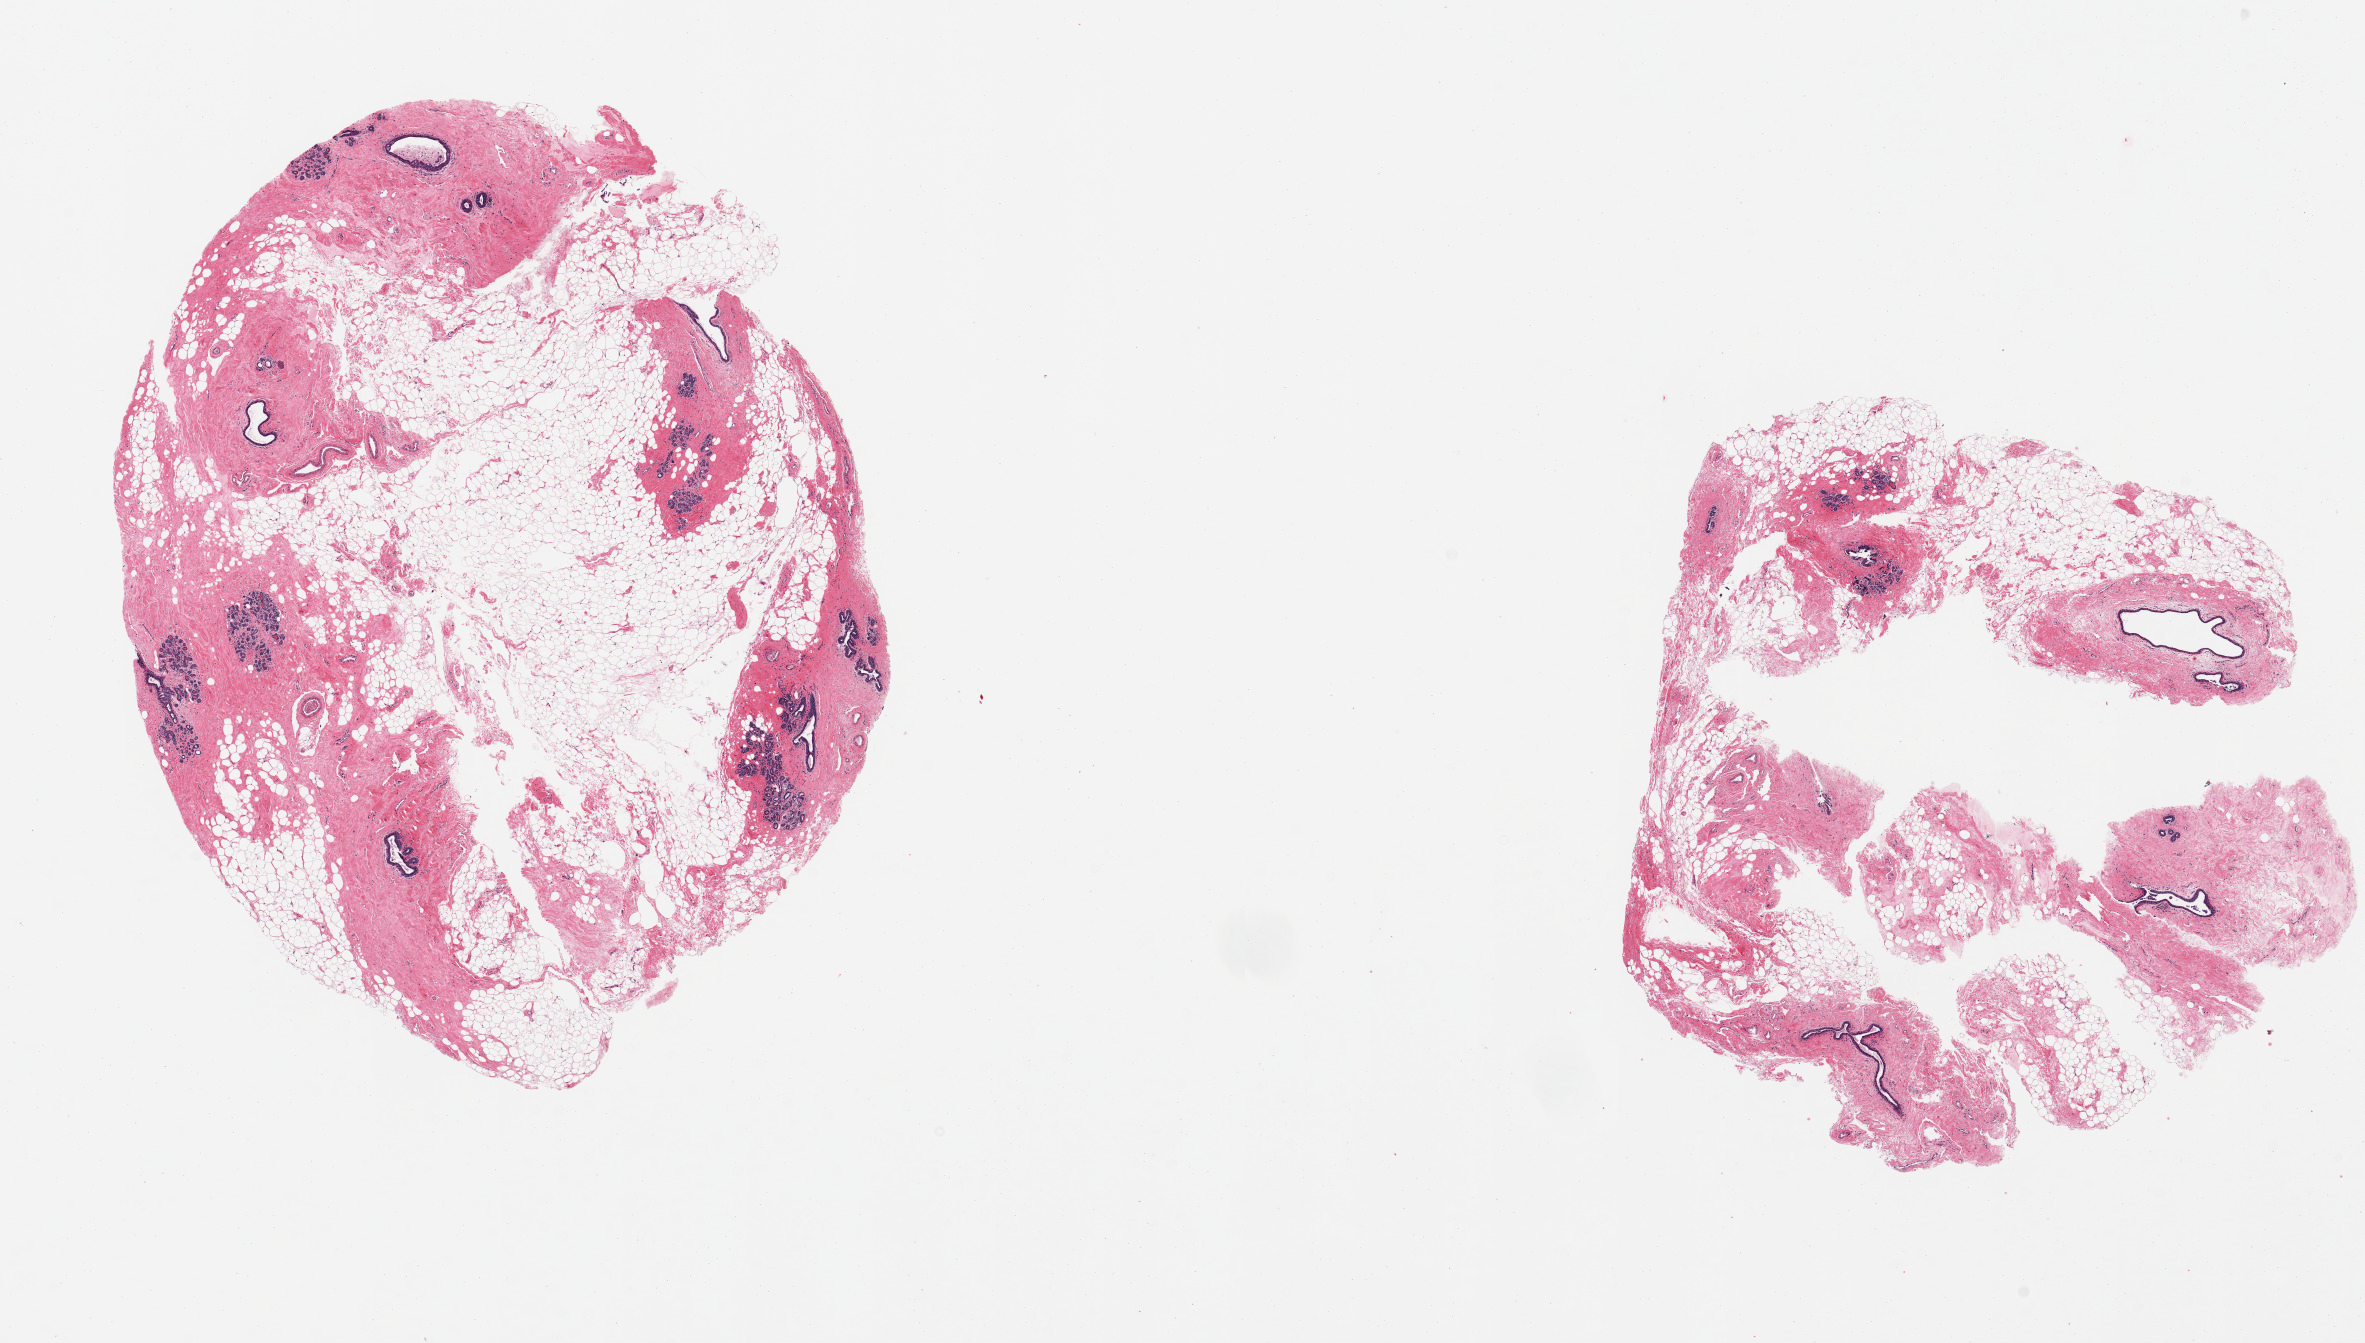
Digitized H&E-stained section — low-resolution overview of the scanned area, about 18.7 x 10.6 mm; PAXgene-fixed paraffin-embedded (PFPE) section; target tissue: breast; tissue donor sample. Female donor.
Pathologist's review note for this sample: 2 pieces; adipose tissue admixed with stroma with ducts and lobules, focal cystic change.